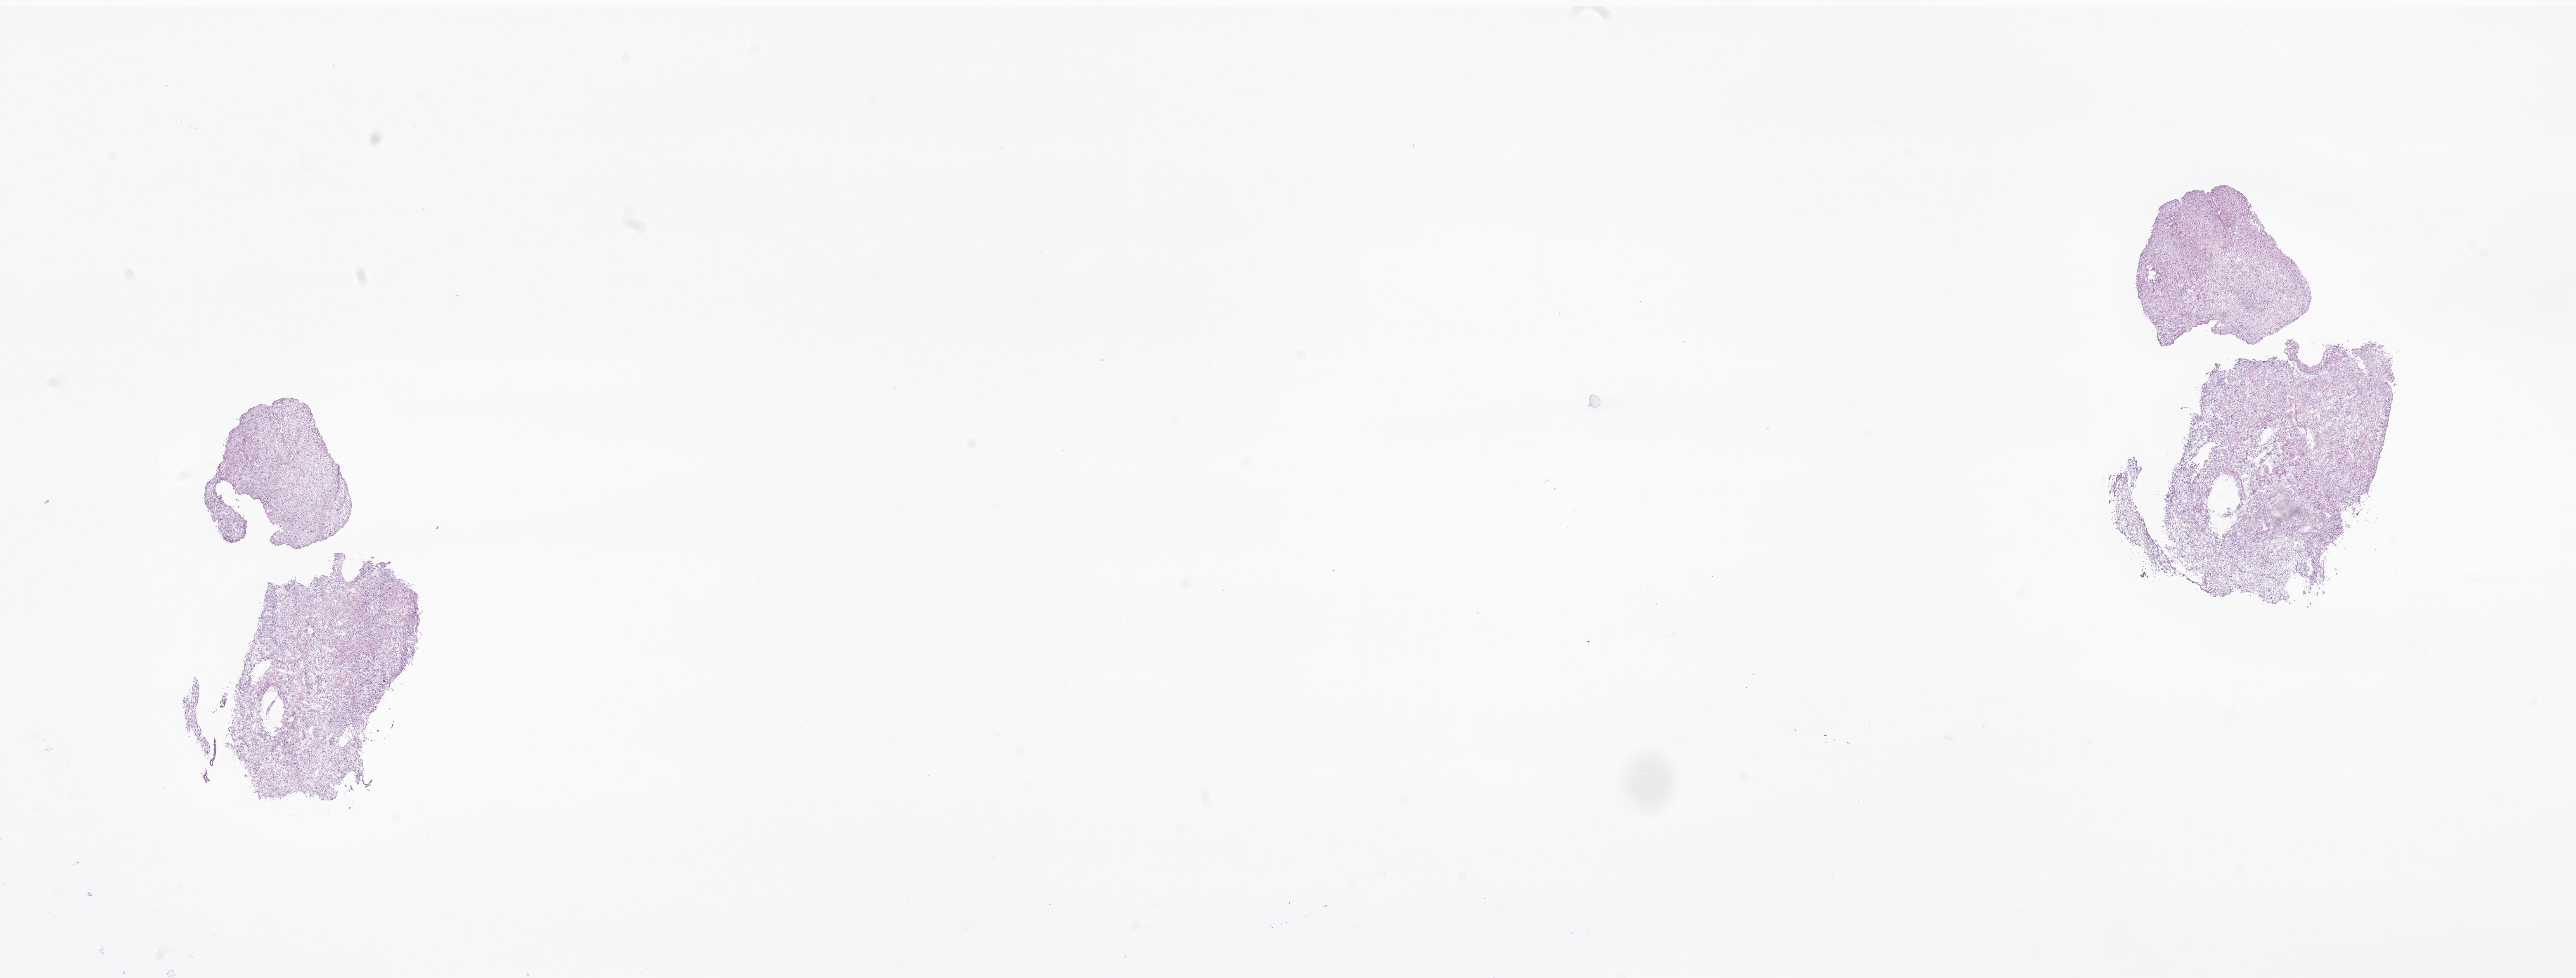
Hematoxylin and eosin (H&E) whole-slide image of tumor tissue from the cerebellum — shown as a low-resolution overview of the whole scanned area (about 26.3 x 10.0 mm); frozen section (OCT-embedded). Patient female; age 110 months (9 years 2 months).
Diagnosis (ICD-O-3 morphology term): Pilocytic astrocytoma.